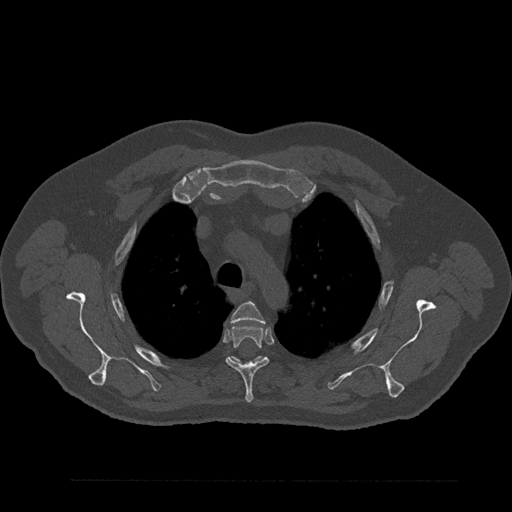
CT including the spine, one axial slice. Slice 645 of 797 in the series (ordered by position). Reconstruction kernel Br40s/3. Bone window (W 1800 / L 400 HU). 0.5 mm slice thickness. 512 × 512 image matrix, field of view 430 × 430 mm. Male patient, age 61 years. Case-level facts recorded for this patient, not image findings: primary cancer: prostate.
Outlined on this slice (semi-automatically segmented with operator editing):
- T3 vertebra: bounding box <231,302,265,323> (left, top, right, bottom; pixels)
- T4 vertebra: <225,325,270,402>
- T5 vertebra: <231,356,265,364>